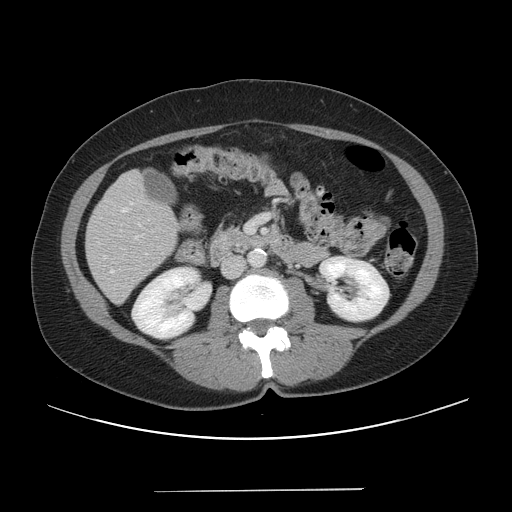
Contrast-enhanced abdominal CT, one axial slice; slice 15 of 56 in the series (ordered by position); soft-tissue window (W 400 / L 40 HU); 5 mm slice thickness; 512 × 512 image matrix, field of view 419 × 419 mm. Female patient, age 54 years. Case-level facts recorded for this patient, not image findings: diagnosis: colorectal cancer liver metastases, imaged before liver resection; multiple liver metastases: yes; largest metastasis: 3.2 cm.
Outlined on this slice (expert manual segmentation):
- liver: box from (x=87, y=172) to (x=178, y=302) px
- portal vein (with intrahepatic branches): (x=247, y=216)–(x=268, y=232)